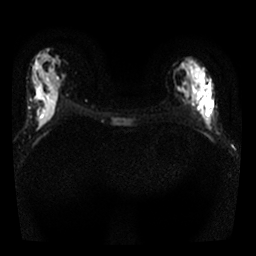
Breast MRI, one axial slice; position 10 of 25 along the scan axis; diffusion-weighted series; image 2 of 4 stored at this slice position (different b-values; order by instance number); 1.5 T; 4 mm slice thickness; 256 × 256 image matrix, field of view 300 × 300 mm. Female patient.
Outlined on this slice (expert manual segmentation):
- tumour on diffusion-weighted imaging: bounding box (x1, y1, x2, y2) in pixels: (199, 83, 217, 127)